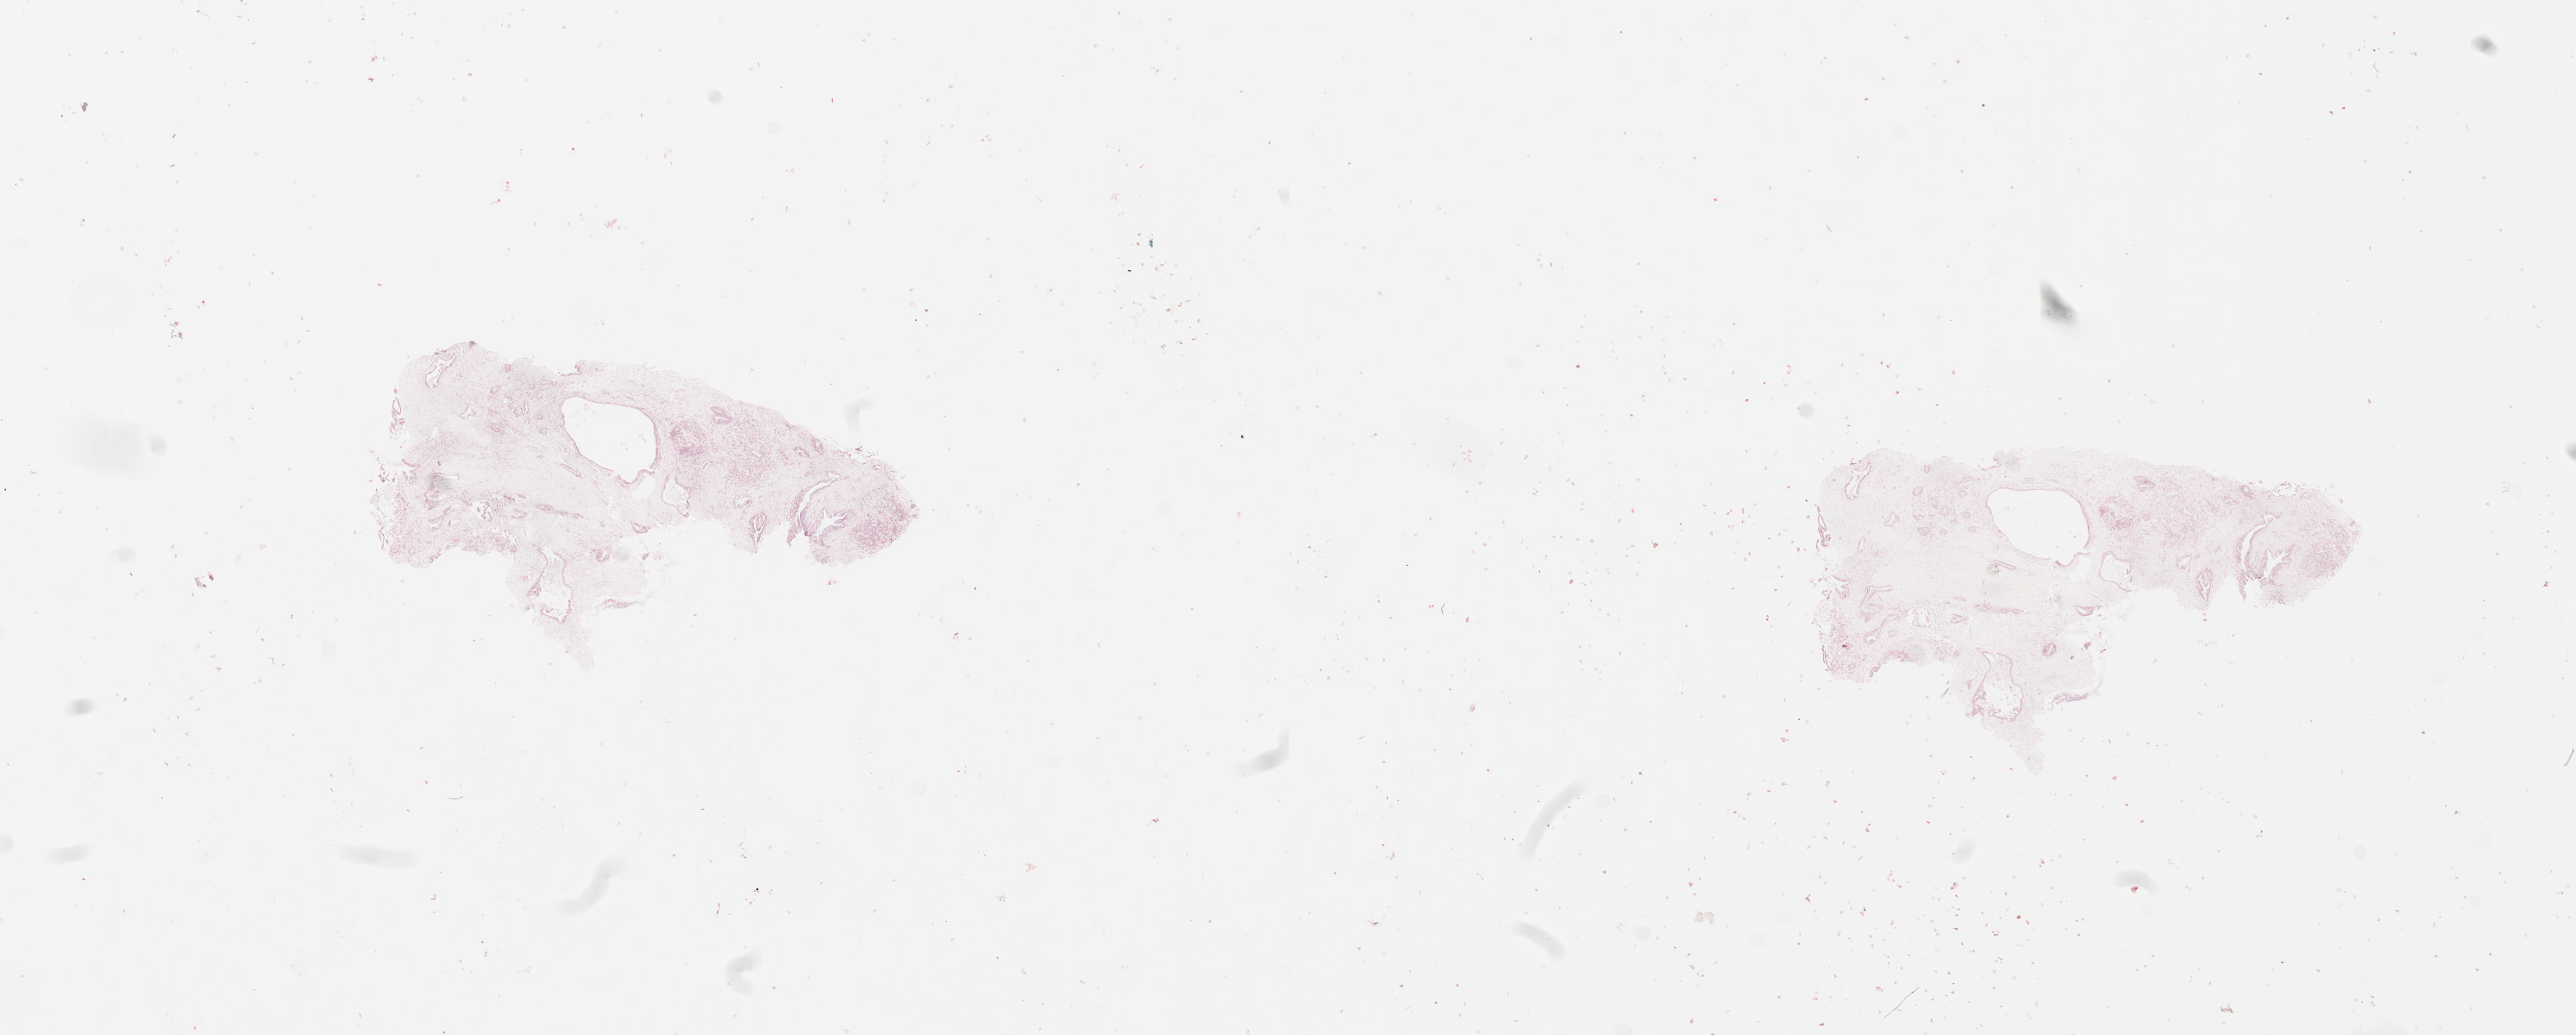
Digitized Hematoxylin and eosin (H&E) stained tissue section (whole slide), shown as a low-resolution overview of the whole scanned area (about 23.6 x 9.5 mm, slide scanned at 20x), tumour tissue sample, sampled site: pancreas. Male, 71 y/o. Histologic grade: G2 (moderately differentiated). Slide review estimates, as recorded: tumour nuclei 10%, necrosis 2%.
AJCC pathologic stage: IIA. Histologic diagnosis: Infiltrating duct carcinoma, NOS. Primary tumour site (as recorded): head.